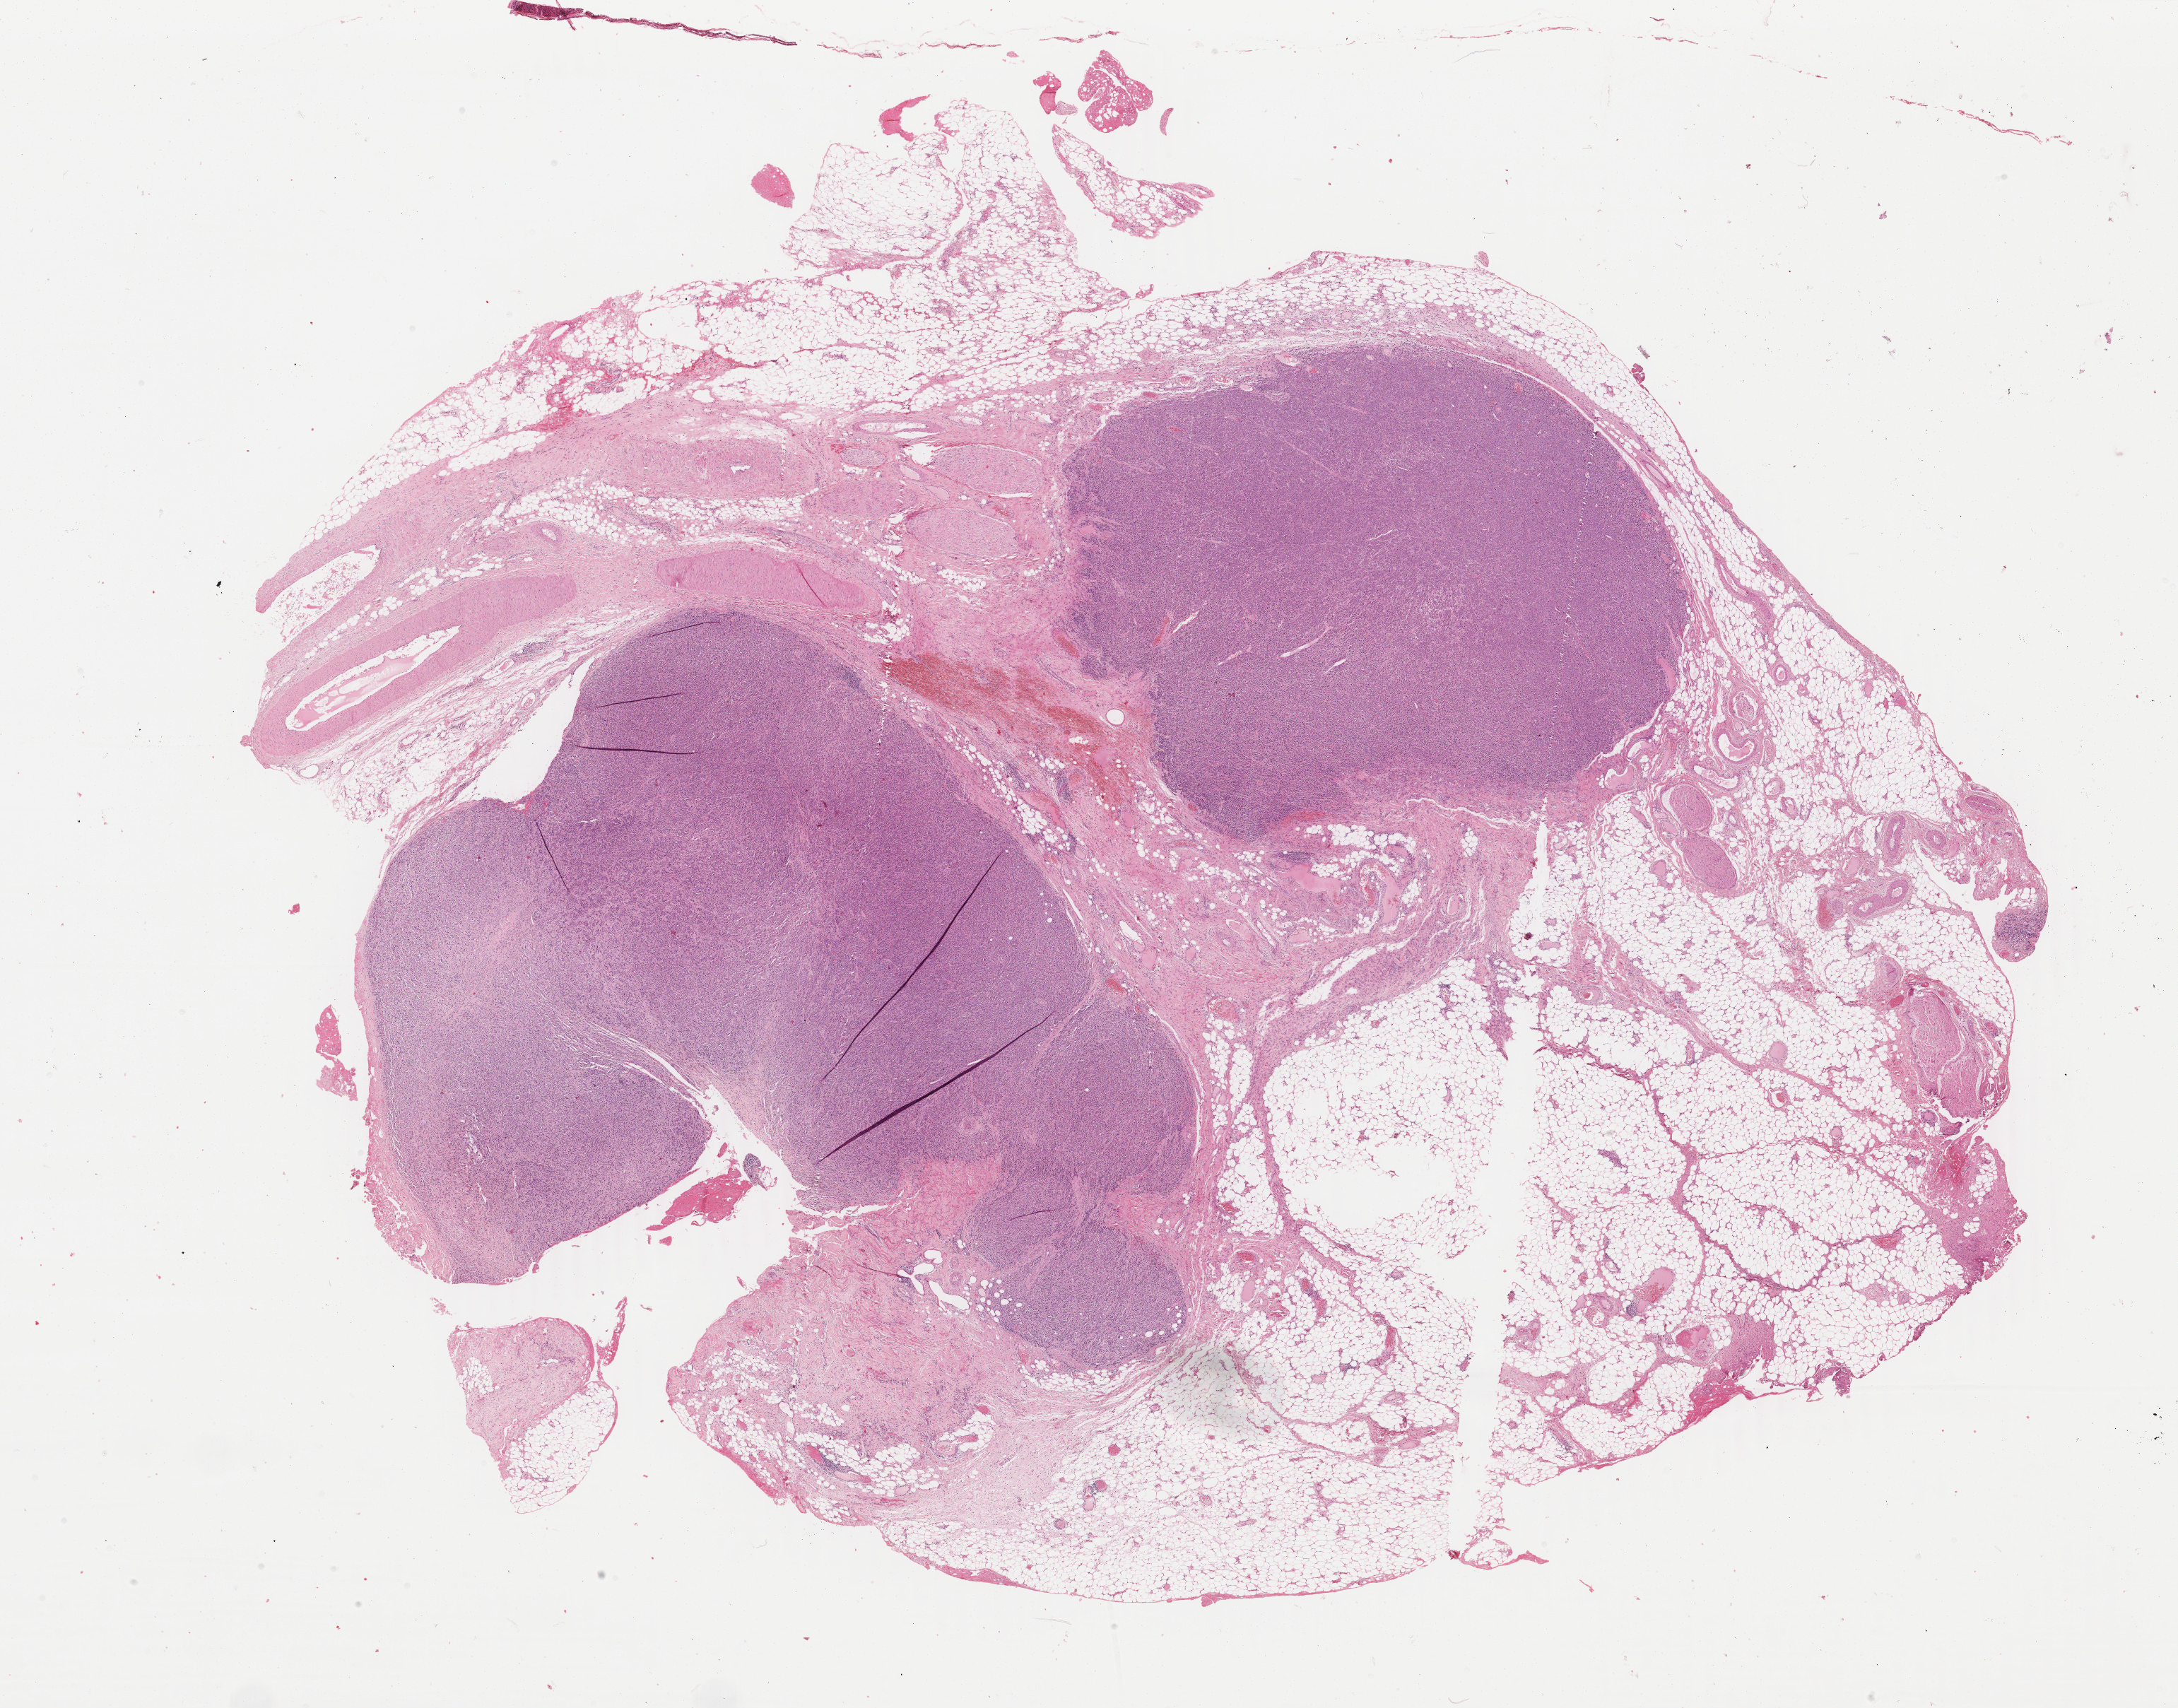
Hematoxylin and eosin (H&E) stained whole-slide image — shown as a low-resolution overview of the whole scanned area (about 24.5 x 19.2 mm, acquisition: 40x scan), formalin-fixed paraffin-embedded (FFPE) diagnostic section, metastatic tumour sample. Patient: female, age at initial diagnosis 77 years.
• this section: metastatic tumour tissue
• patient diagnosis: Malignant melanoma, NOS